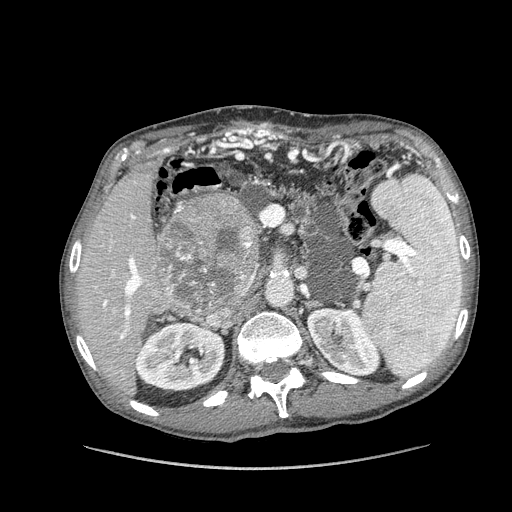
Contrast-enhanced abdominal CT (liver protocol), one axial slice; slice 69 of 162 in the series (ordered by position); reconstruction kernel STANDARD; soft-tissue window (W 400 / L 40 HU); 2.5 mm slice thickness; 512 × 512 image matrix. Case-level facts recorded for this patient, not image findings: diagnosis: hepatocellular carcinoma (patient treated with transarterial chemoembolisation; whether this scan precedes or follows treatment is not stated here); TNM stage (as recorded): Stage-IIIA.
Outlined on this slice (semi-automatic segmentation, software-assisted and operator-edited):
- liver parenchyma outside the tumour (the mass and vessels are separate outlines, so this box may not span the whole liver): bounding box [x1, y1, x2, y2] px = [76, 162, 259, 394]
- mass: [155, 197, 261, 313]
- liver vessels: [101, 214, 143, 339]